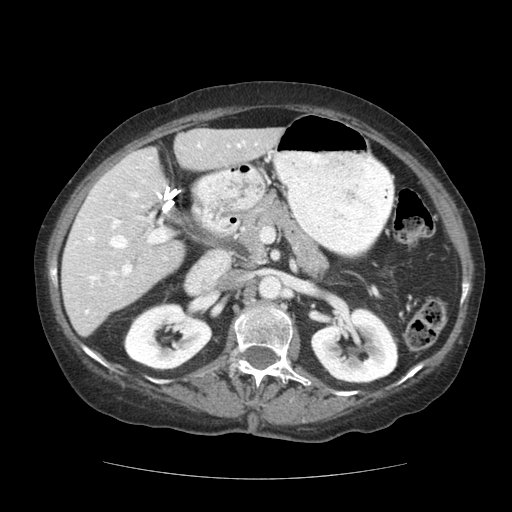
Contrast-enhanced abdominal CT (liver protocol), one axial slice; position 65 of 111 along the scan axis; reconstruction kernel STANDARD; soft-tissue window (W 400 / L 40 HU); 2.5 mm slice thickness; 512 × 512 image matrix, field of view 360 × 360 mm. From the clinical record (not read from this slice): diagnosis: hepatocellular carcinoma (patient treated with transarterial chemoembolisation; whether this scan precedes or follows treatment is not stated here); TNM stage (as recorded): Stage-I.
Structures marked on this image (semi-automatic segmentation, software-assisted and operator-edited):
- liver parenchyma outside the tumour (the mass and vessels are separate outlines, so this box may not span the whole liver): bounding box <62,128,282,336> (left, top, right, bottom; pixels)
- liver vessels: <72,140,257,314>